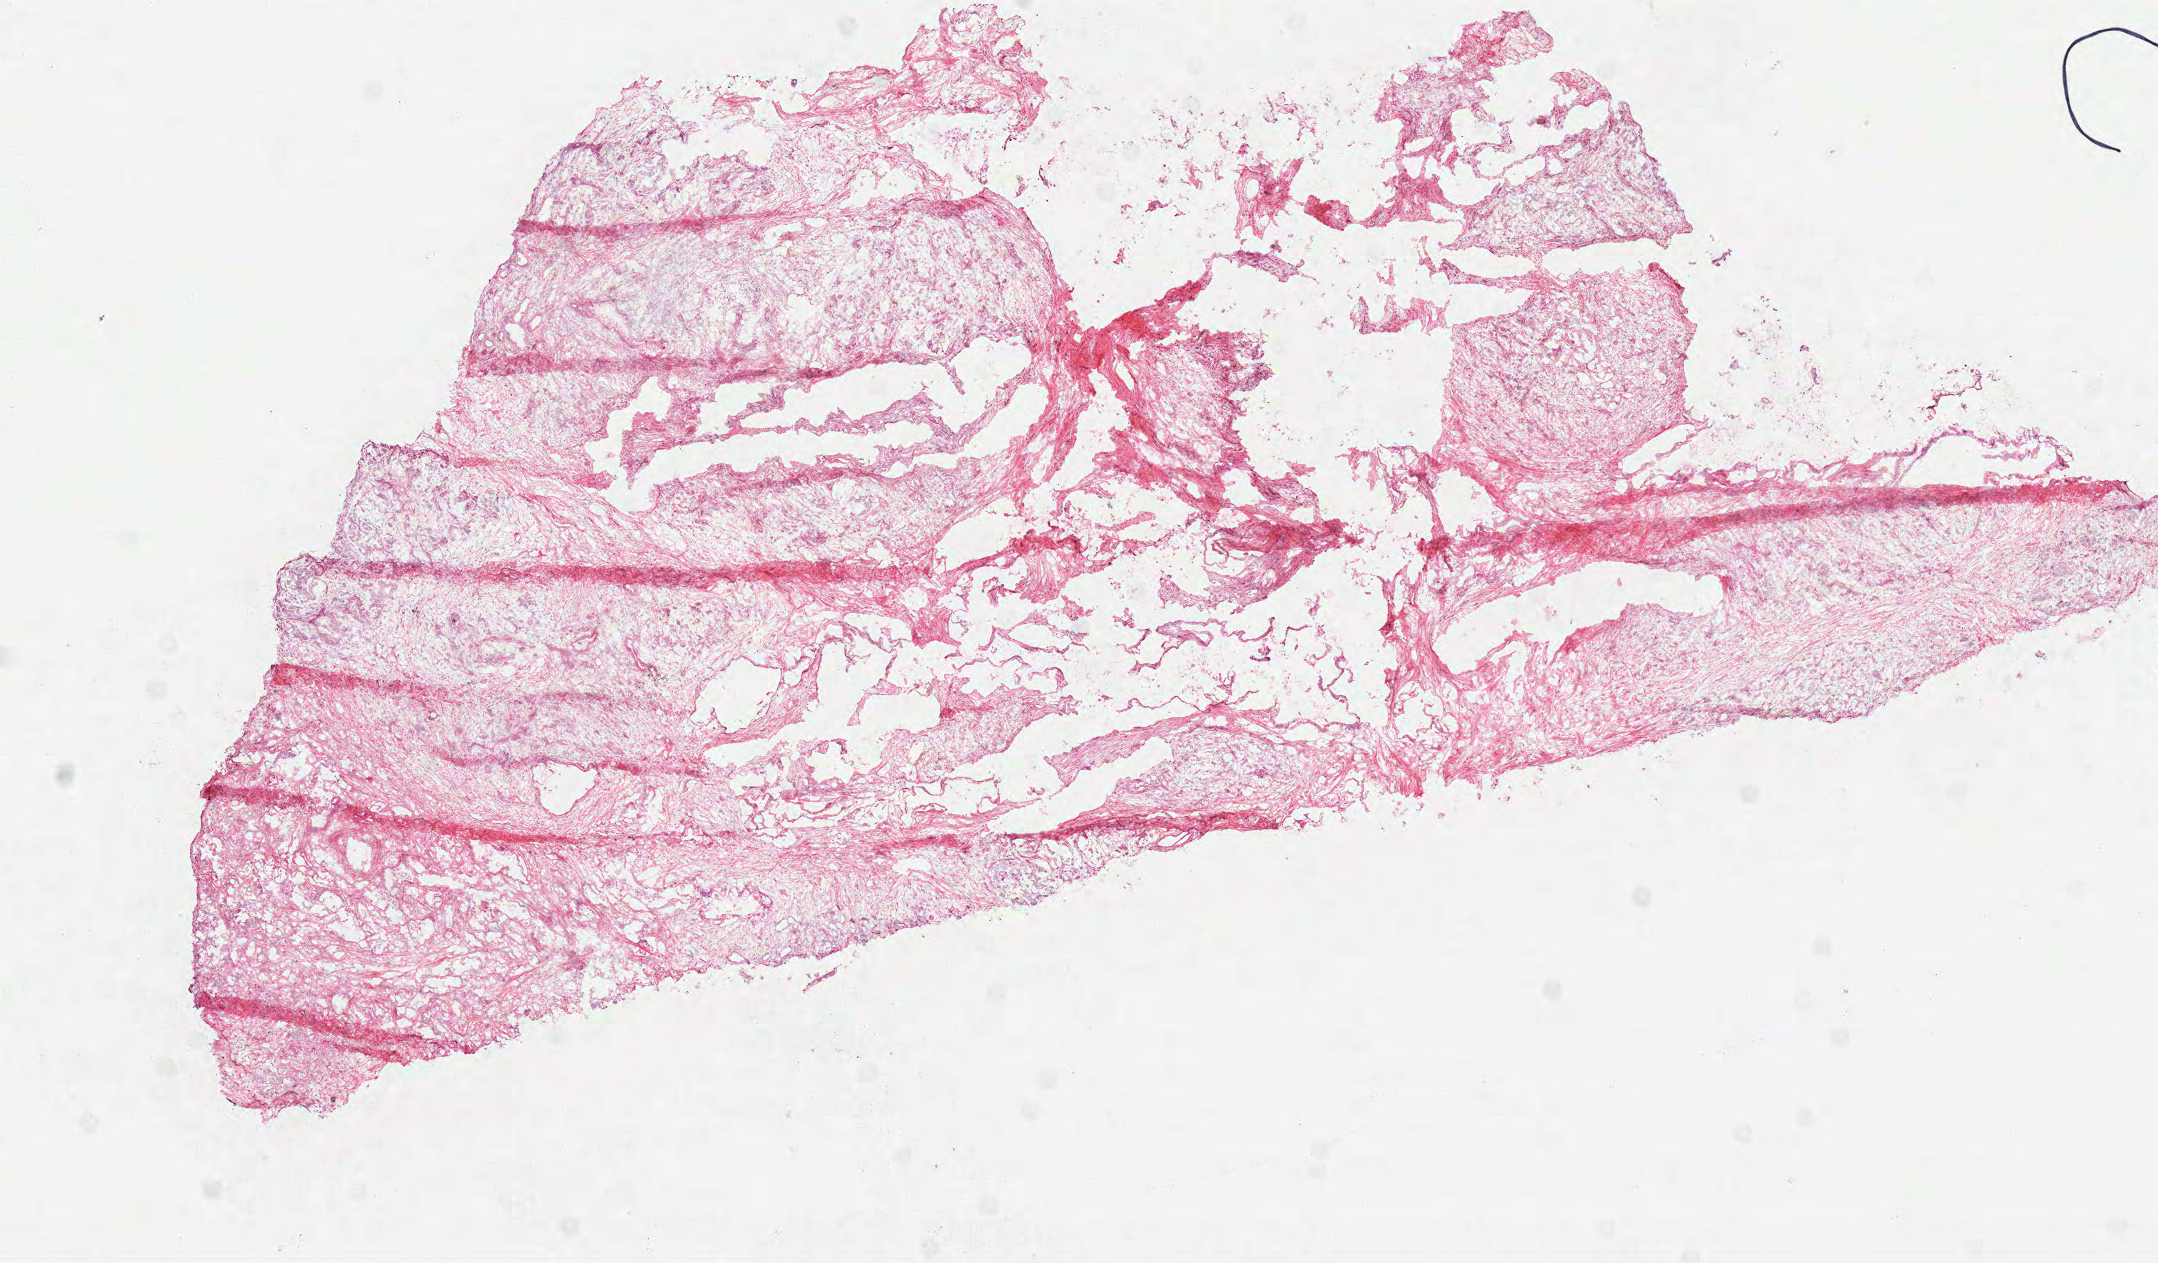
Digitized H&E tissue section (whole slide) — a low-resolution overview of the entire scanned area, about 8.7 x 5.1 mm (from a 40x scan), frozen section from the top of the tissue portion, primary tumour sample from the pancreas. Female, age 73 years at initial diagnosis. Histologic grade: G2 (moderately differentiated). Pathologist review of this section (percent, as recorded): tumour cells 100%, tumour nuclei 77%, normal cells 0%, stromal cells 0%, necrosis 0%. Infiltration values recorded for this section: lymphocyte infiltration 5%, monocyte infiltration 0%, neutrophil infiltration 0%.
AJCC pathologic stage: IIB. Pathologic diagnosis: Infiltrating duct carcinoma, NOS (head of pancreas). Lymph nodes positive (case pathology): 5 of 13 examined.